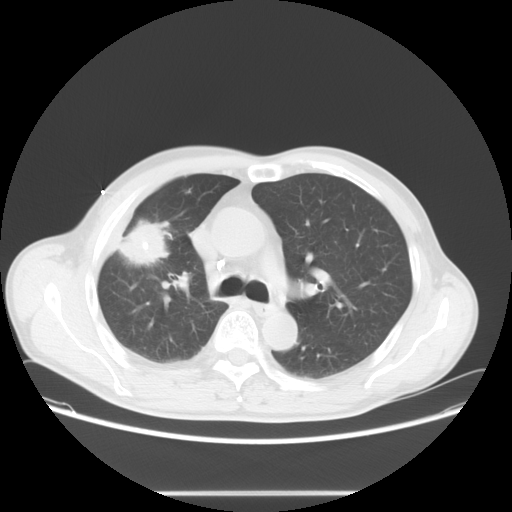
Chest CT, one axial slice; slice 46 of 71 in the series (ordered by position); reconstruction kernel STANDARD; lung window (W 1500 / L -600 HU); 5 mm slice thickness; 512 × 512 image matrix, field of view 392 × 392 mm. Male patient, age 67 years. From the clinical record (not read from this slice): clinical TNM (as recorded): T2 N0 M0.
Structures marked on this image (rectangle marked by the reading radiologist):
- lung tumour (recorded histology: adenocarcinoma): box from (x=122, y=215) to (x=169, y=271) px